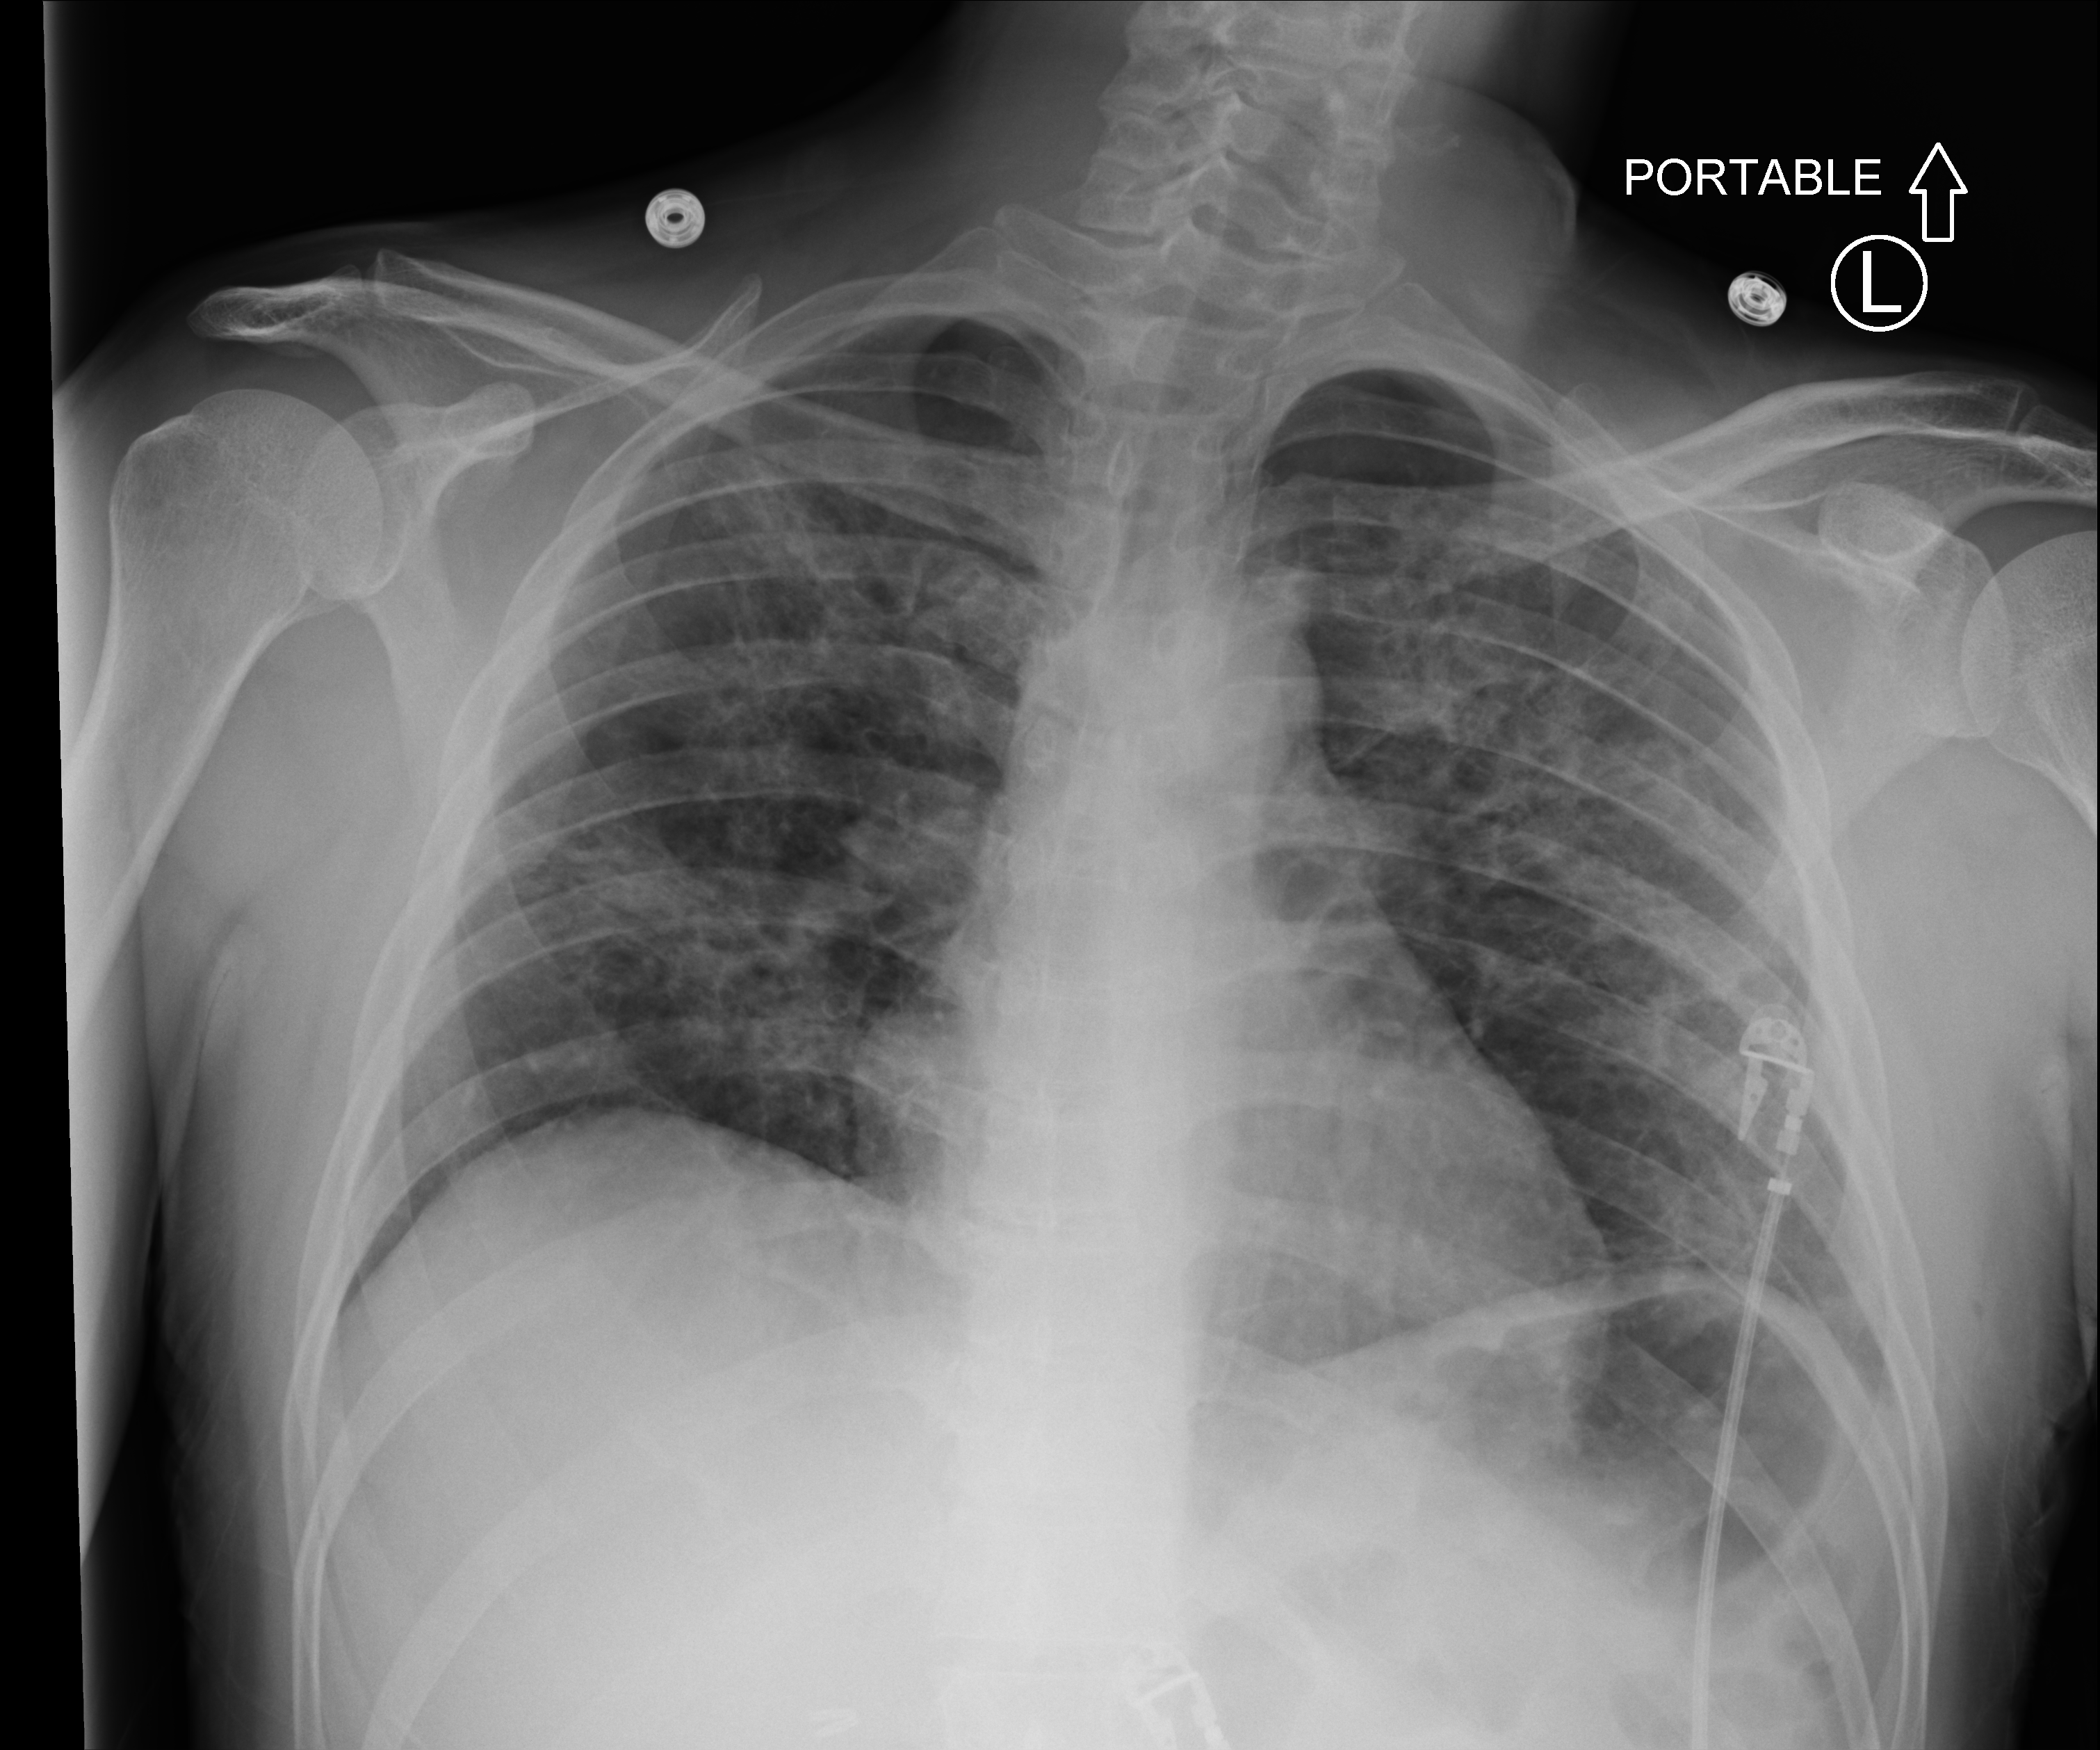
Chest X-ray (portable), anteroposterior (AP) projection. Male patient hospitalised with COVID-19, age 18–59 years.
Admission-level facts for this patient (not findings on this image; timing relative to this image not recorded): diabetes (admission record): no; hypertension (admission record): no.